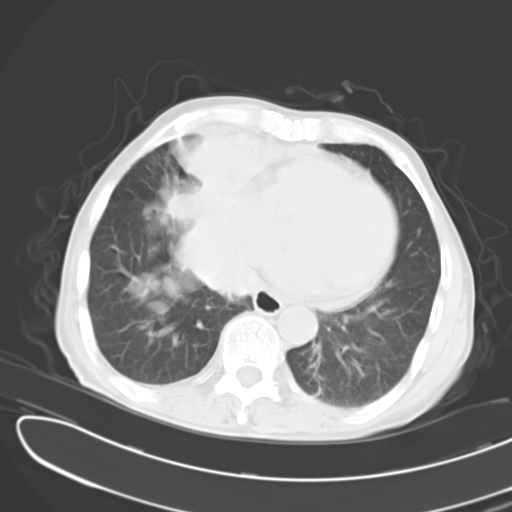
Chest CT, one axial slice; slice 6 of 24 in the series (ordered by position); reconstruction kernel B40f; lung window (W 1500 / L -600 HU); 512 × 512 image matrix. Male patient, age 65 years. Case-level facts recorded for this patient, not image findings: clinical TNM (as recorded): T2 N3 M1; histopathological grade: G3.
Outlined on this slice (bounding box drawn by a radiologist):
- lung tumour (recorded histology: small cell carcinoma): bounding box [x1, y1, x2, y2] px = [147, 106, 276, 305]